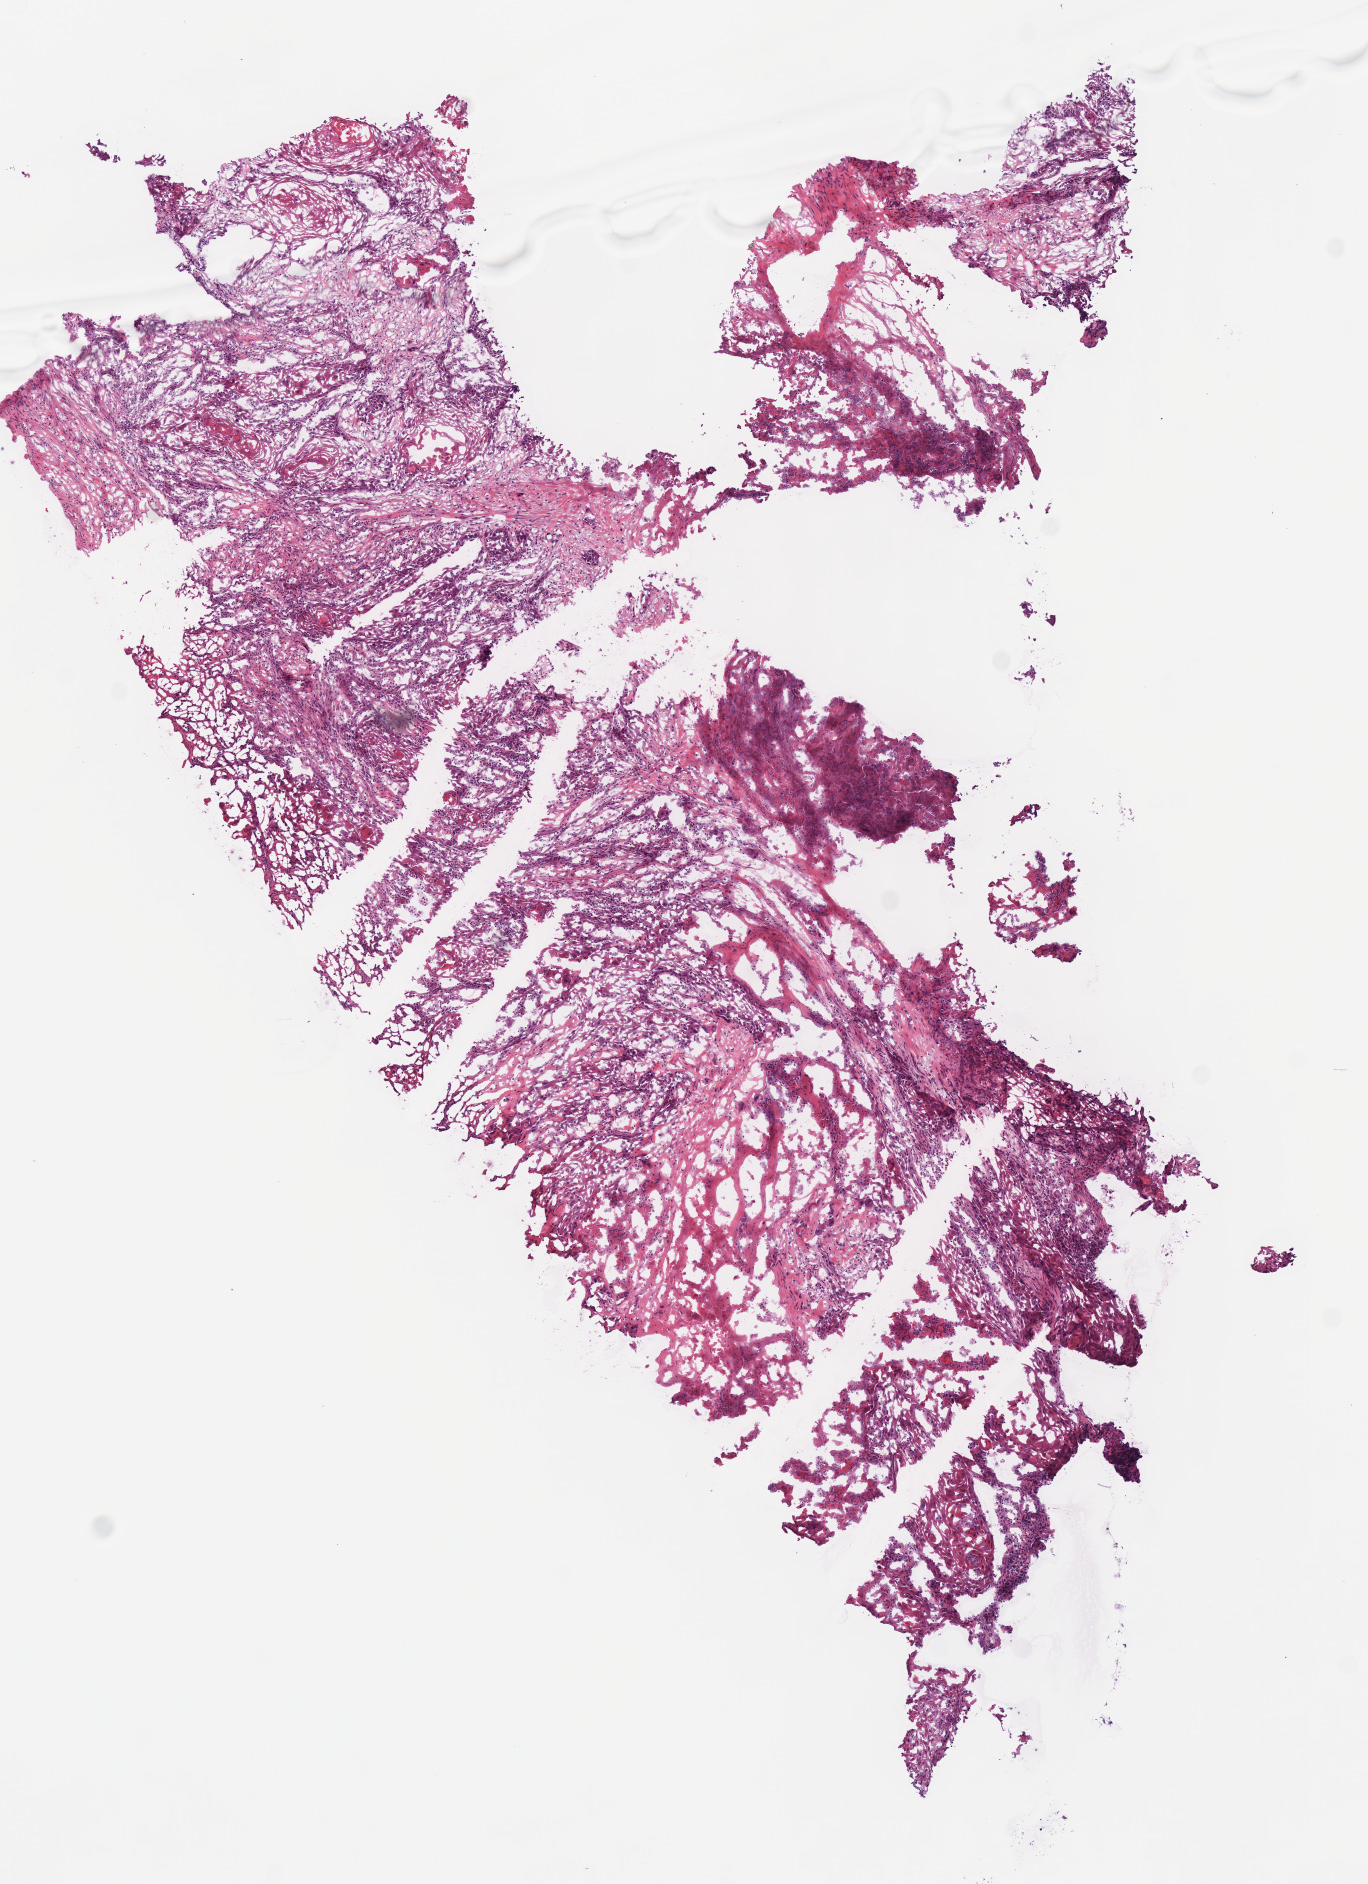
Whole-slide histology image, H&E-stained — low-resolution overview of the scanned area, about 5.4 x 7.4 mm (from a 40x scan). Frozen section from the bottom of the tissue portion. Head and neck, primary tumour sample. Patient: male, age at initial diagnosis 49 years. Histologic grade: G3 (poorly differentiated). Pathologist review of this section (percent, as recorded): tumour cells 65%, tumour nuclei 70%, normal cells 0%, stromal cells 25%, necrosis 10%.
* pathologic diagnosis: Squamous cell carcinoma, NOS (larynx, NOS)
* AJCC pathologic stage: IVA